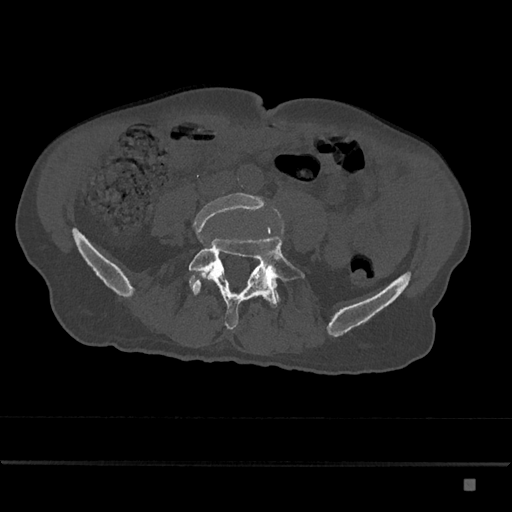
CT including the spine, one axial slice; 120 kVp; bone window (W 1800 / L 400 HU); 0.5 mm slice thickness; 512 × 512 image matrix, field of view 390 × 390 mm. Patient: male, 72 years. Case-level facts recorded for this patient, not image findings: primary cancer: prostate.
Outlined on this slice (semi-automatically segmented with operator editing):
- L4 vertebra: bounding box [x1, y1, x2, y2] px = [193, 193, 267, 280]
- L5 vertebra: [189, 228, 305, 330]